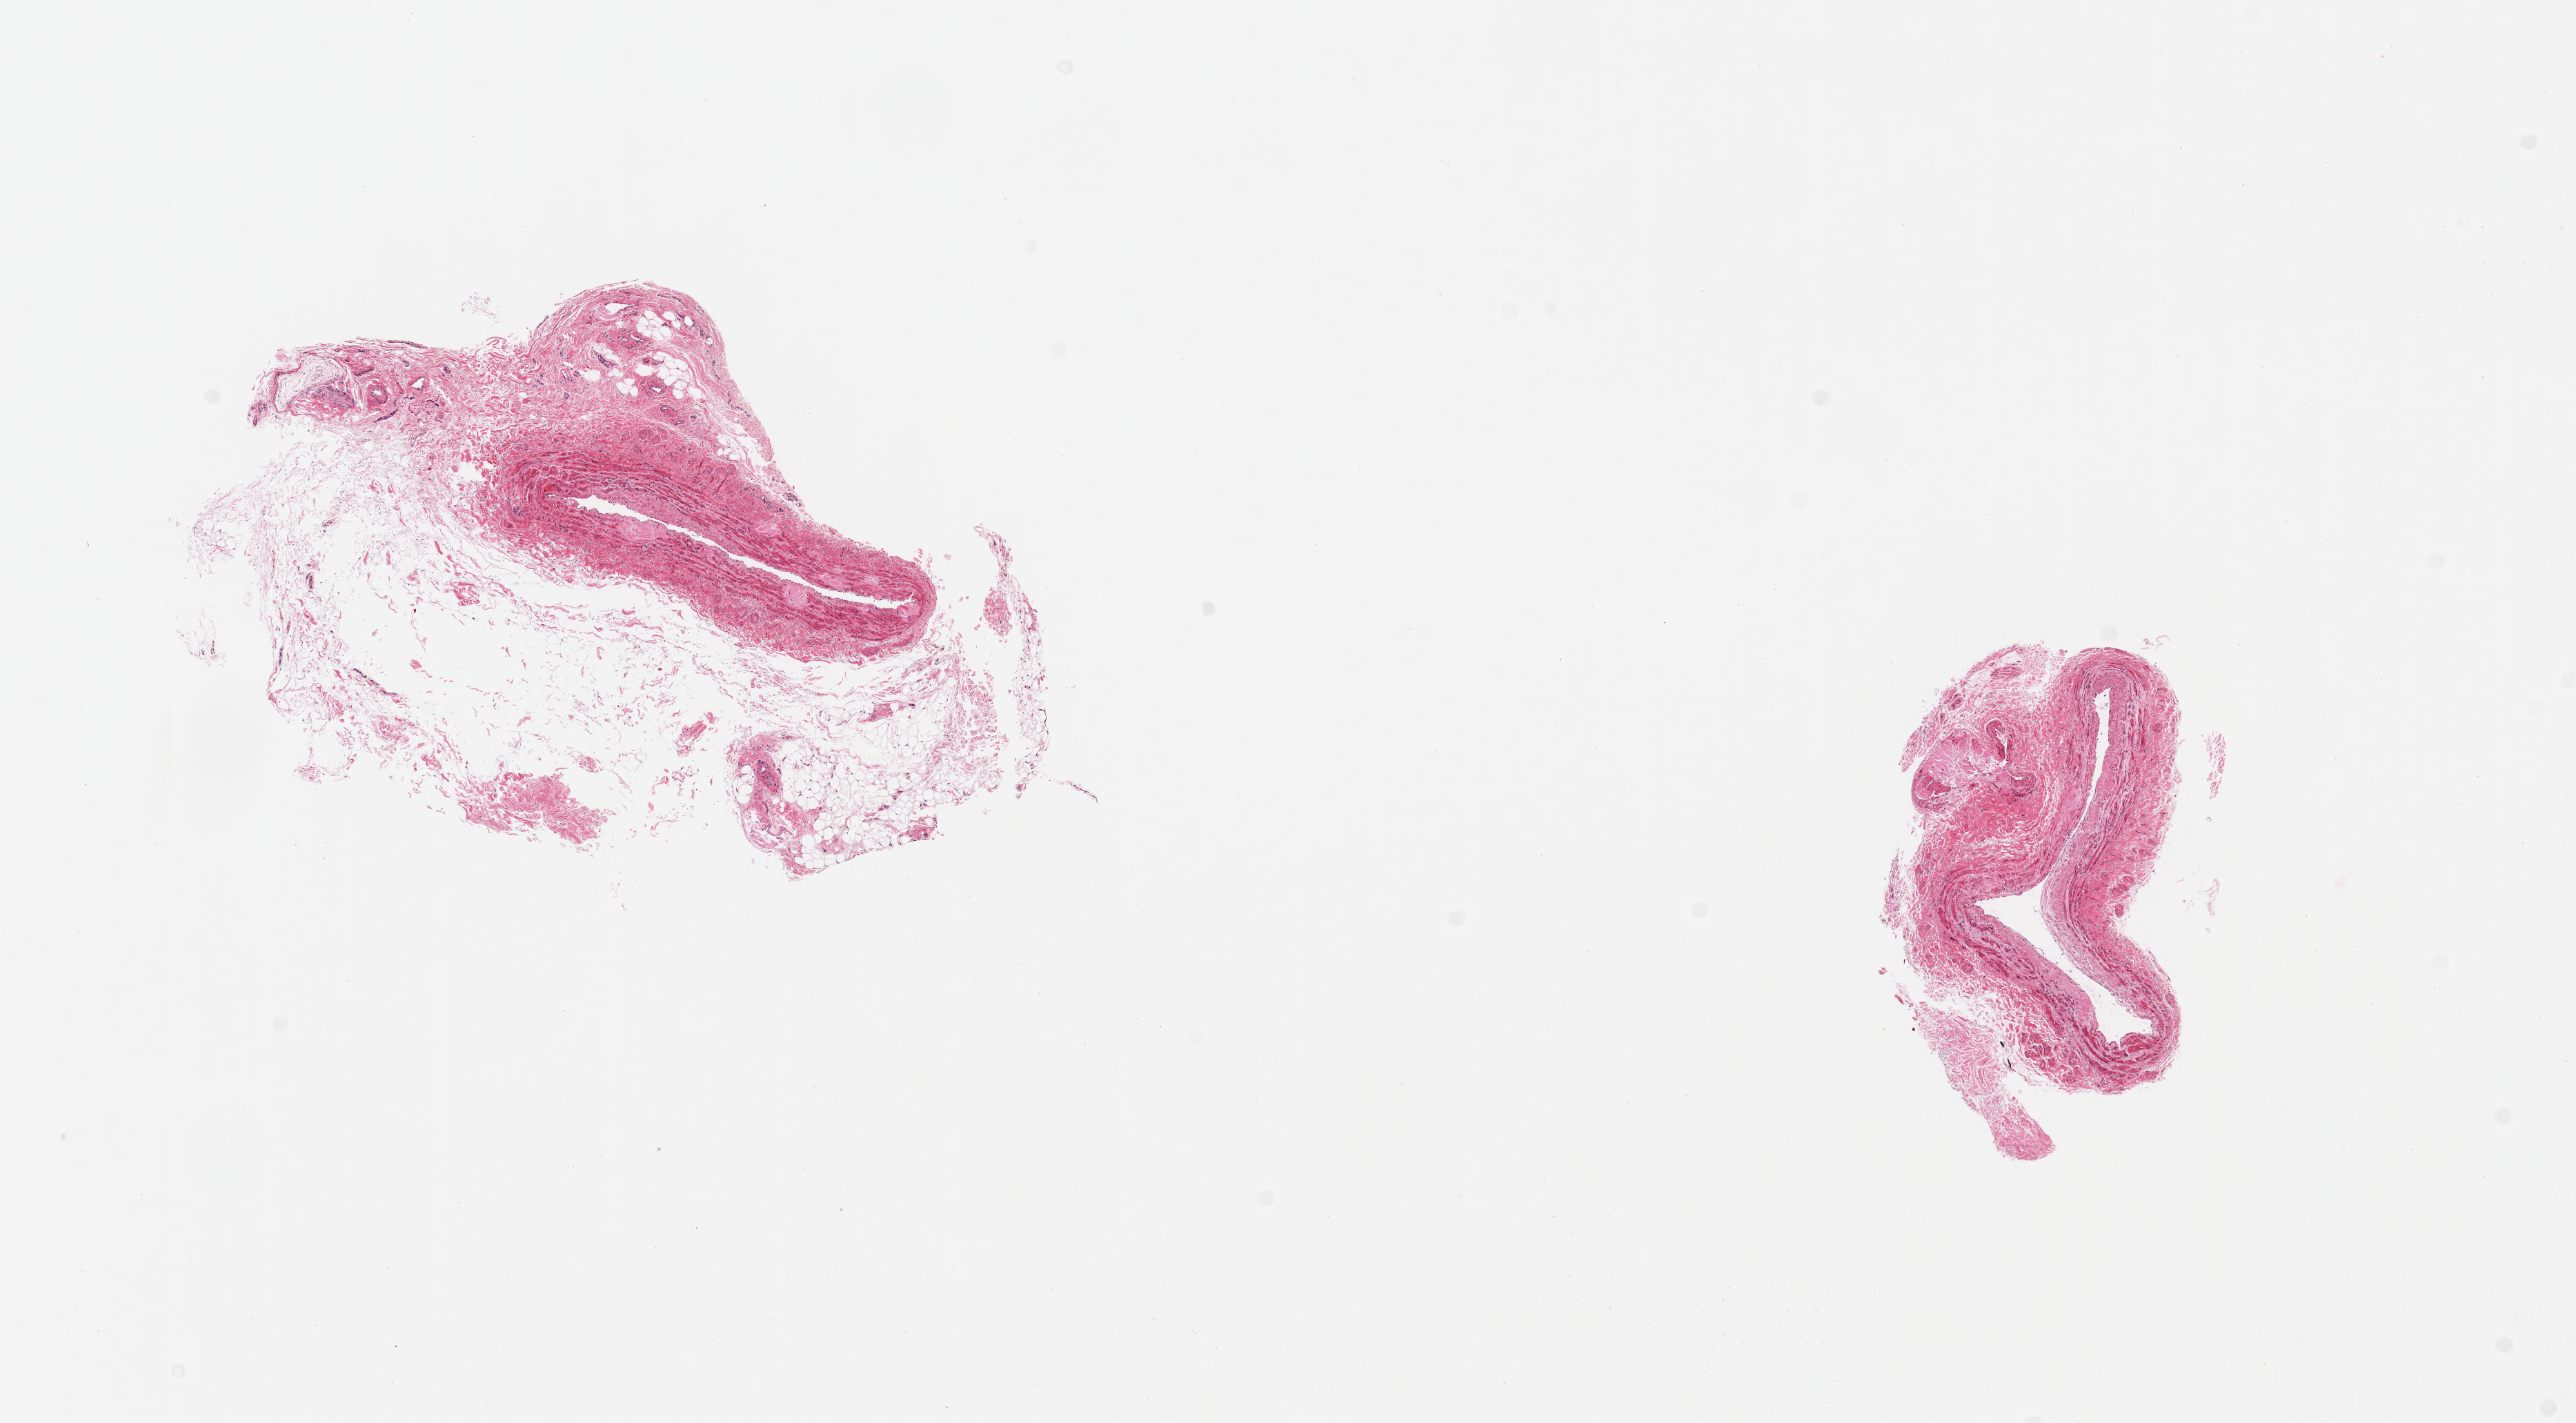
Whole-slide image, H&E stain — low-resolution overview of the scanned area, about 14.8 x 8.2 mm (from a 20x scan); PAXgene-fixed, paraffin-embedded tissue; sampled site (target tissue): tibial artery; donor tissue sample. Donor: female.
Review note (as recorded): 2 pieces; external fat comprises 70% area in 1 piece; mild plaque formation.